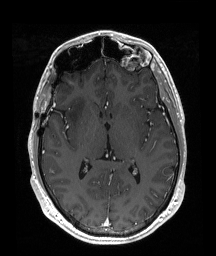
Brain MRI from a brain-tumour surgery series, one axial slice. T1-weighted post-contrast. 216 × 256 image matrix. Case-level facts recorded for this patient, not image findings: histopathology: Astrocytoma; WHO grade: 2; IDH mutation: yes.
Structures marked on this image (outlined manually by an expert reader):
- tumour: bounding box [x1, y1, x2, y2] px = [68, 96, 88, 129]